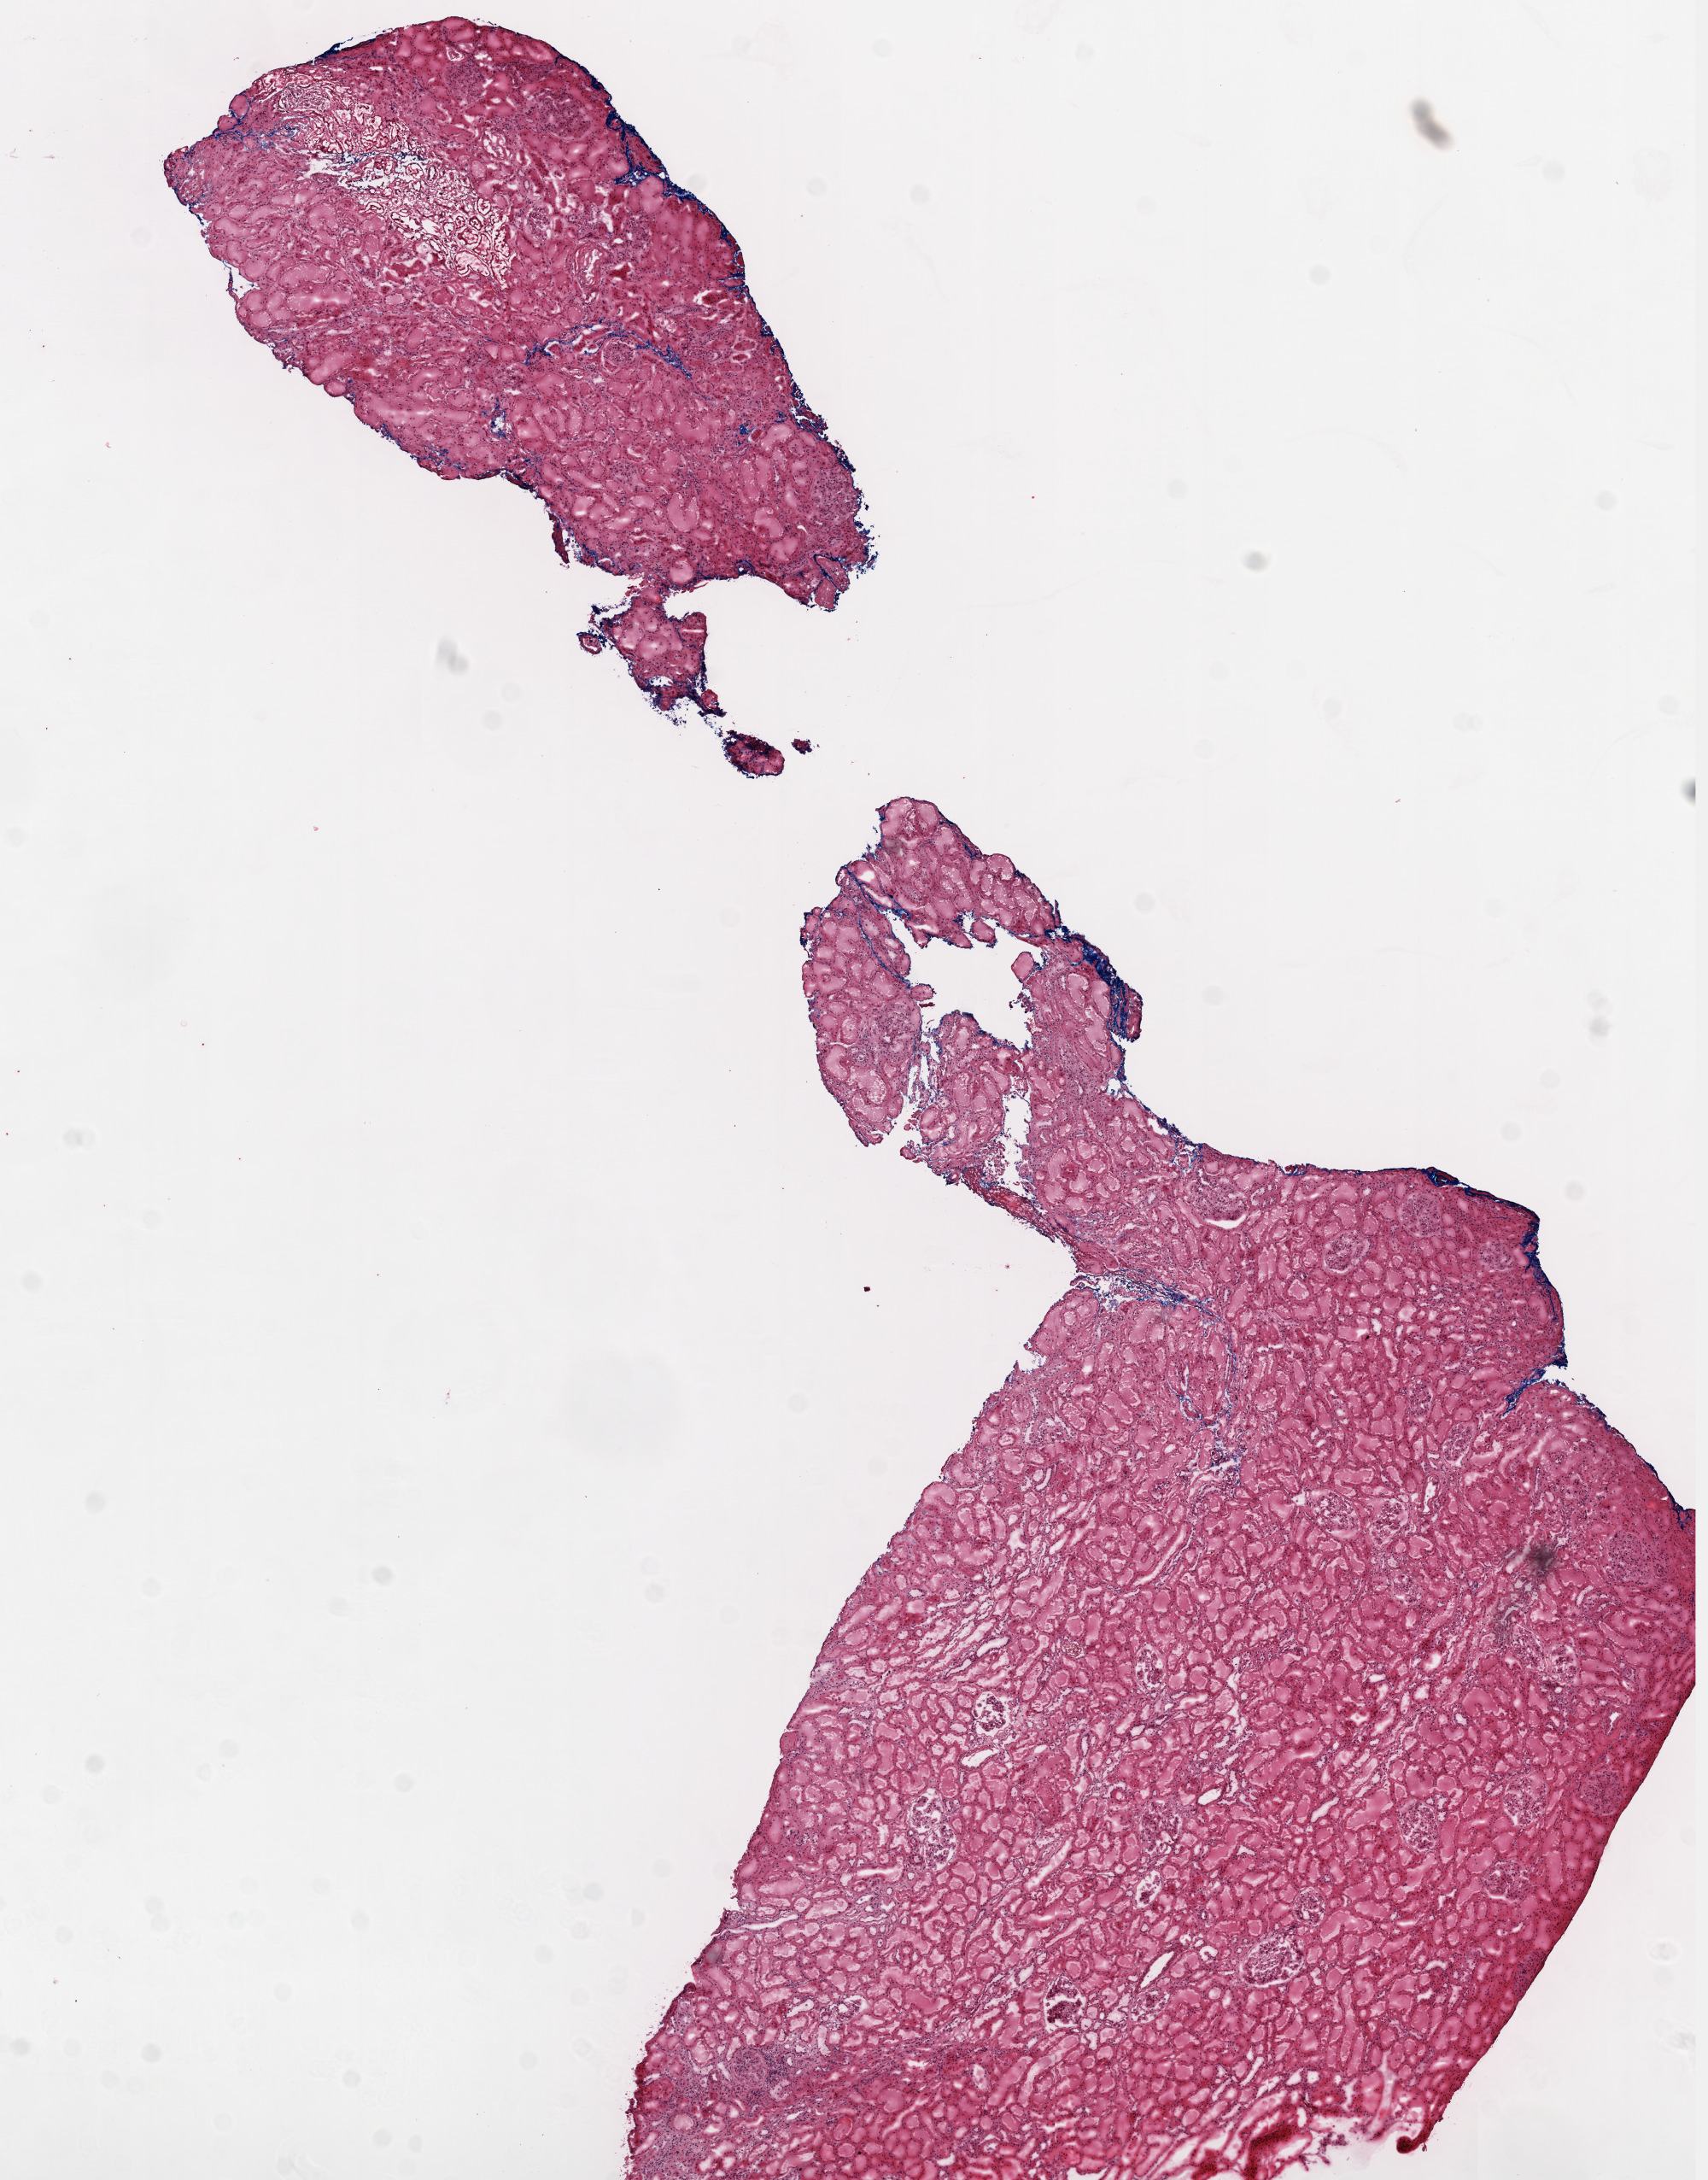
H&E whole-slide image — whole scanned area (about 8.0 x 10.2 mm, slide scanned at 20x) shown as a low-resolution overview, frozen section from the top of the tissue portion, kidney, solid tissue normal (non-tumour tissue) sample. Patient: female, age at initial diagnosis 67 years.
This section: solid tissue normal sample (biorepository sample class). Patient diagnosis: Clear cell adenocarcinoma, NOS.